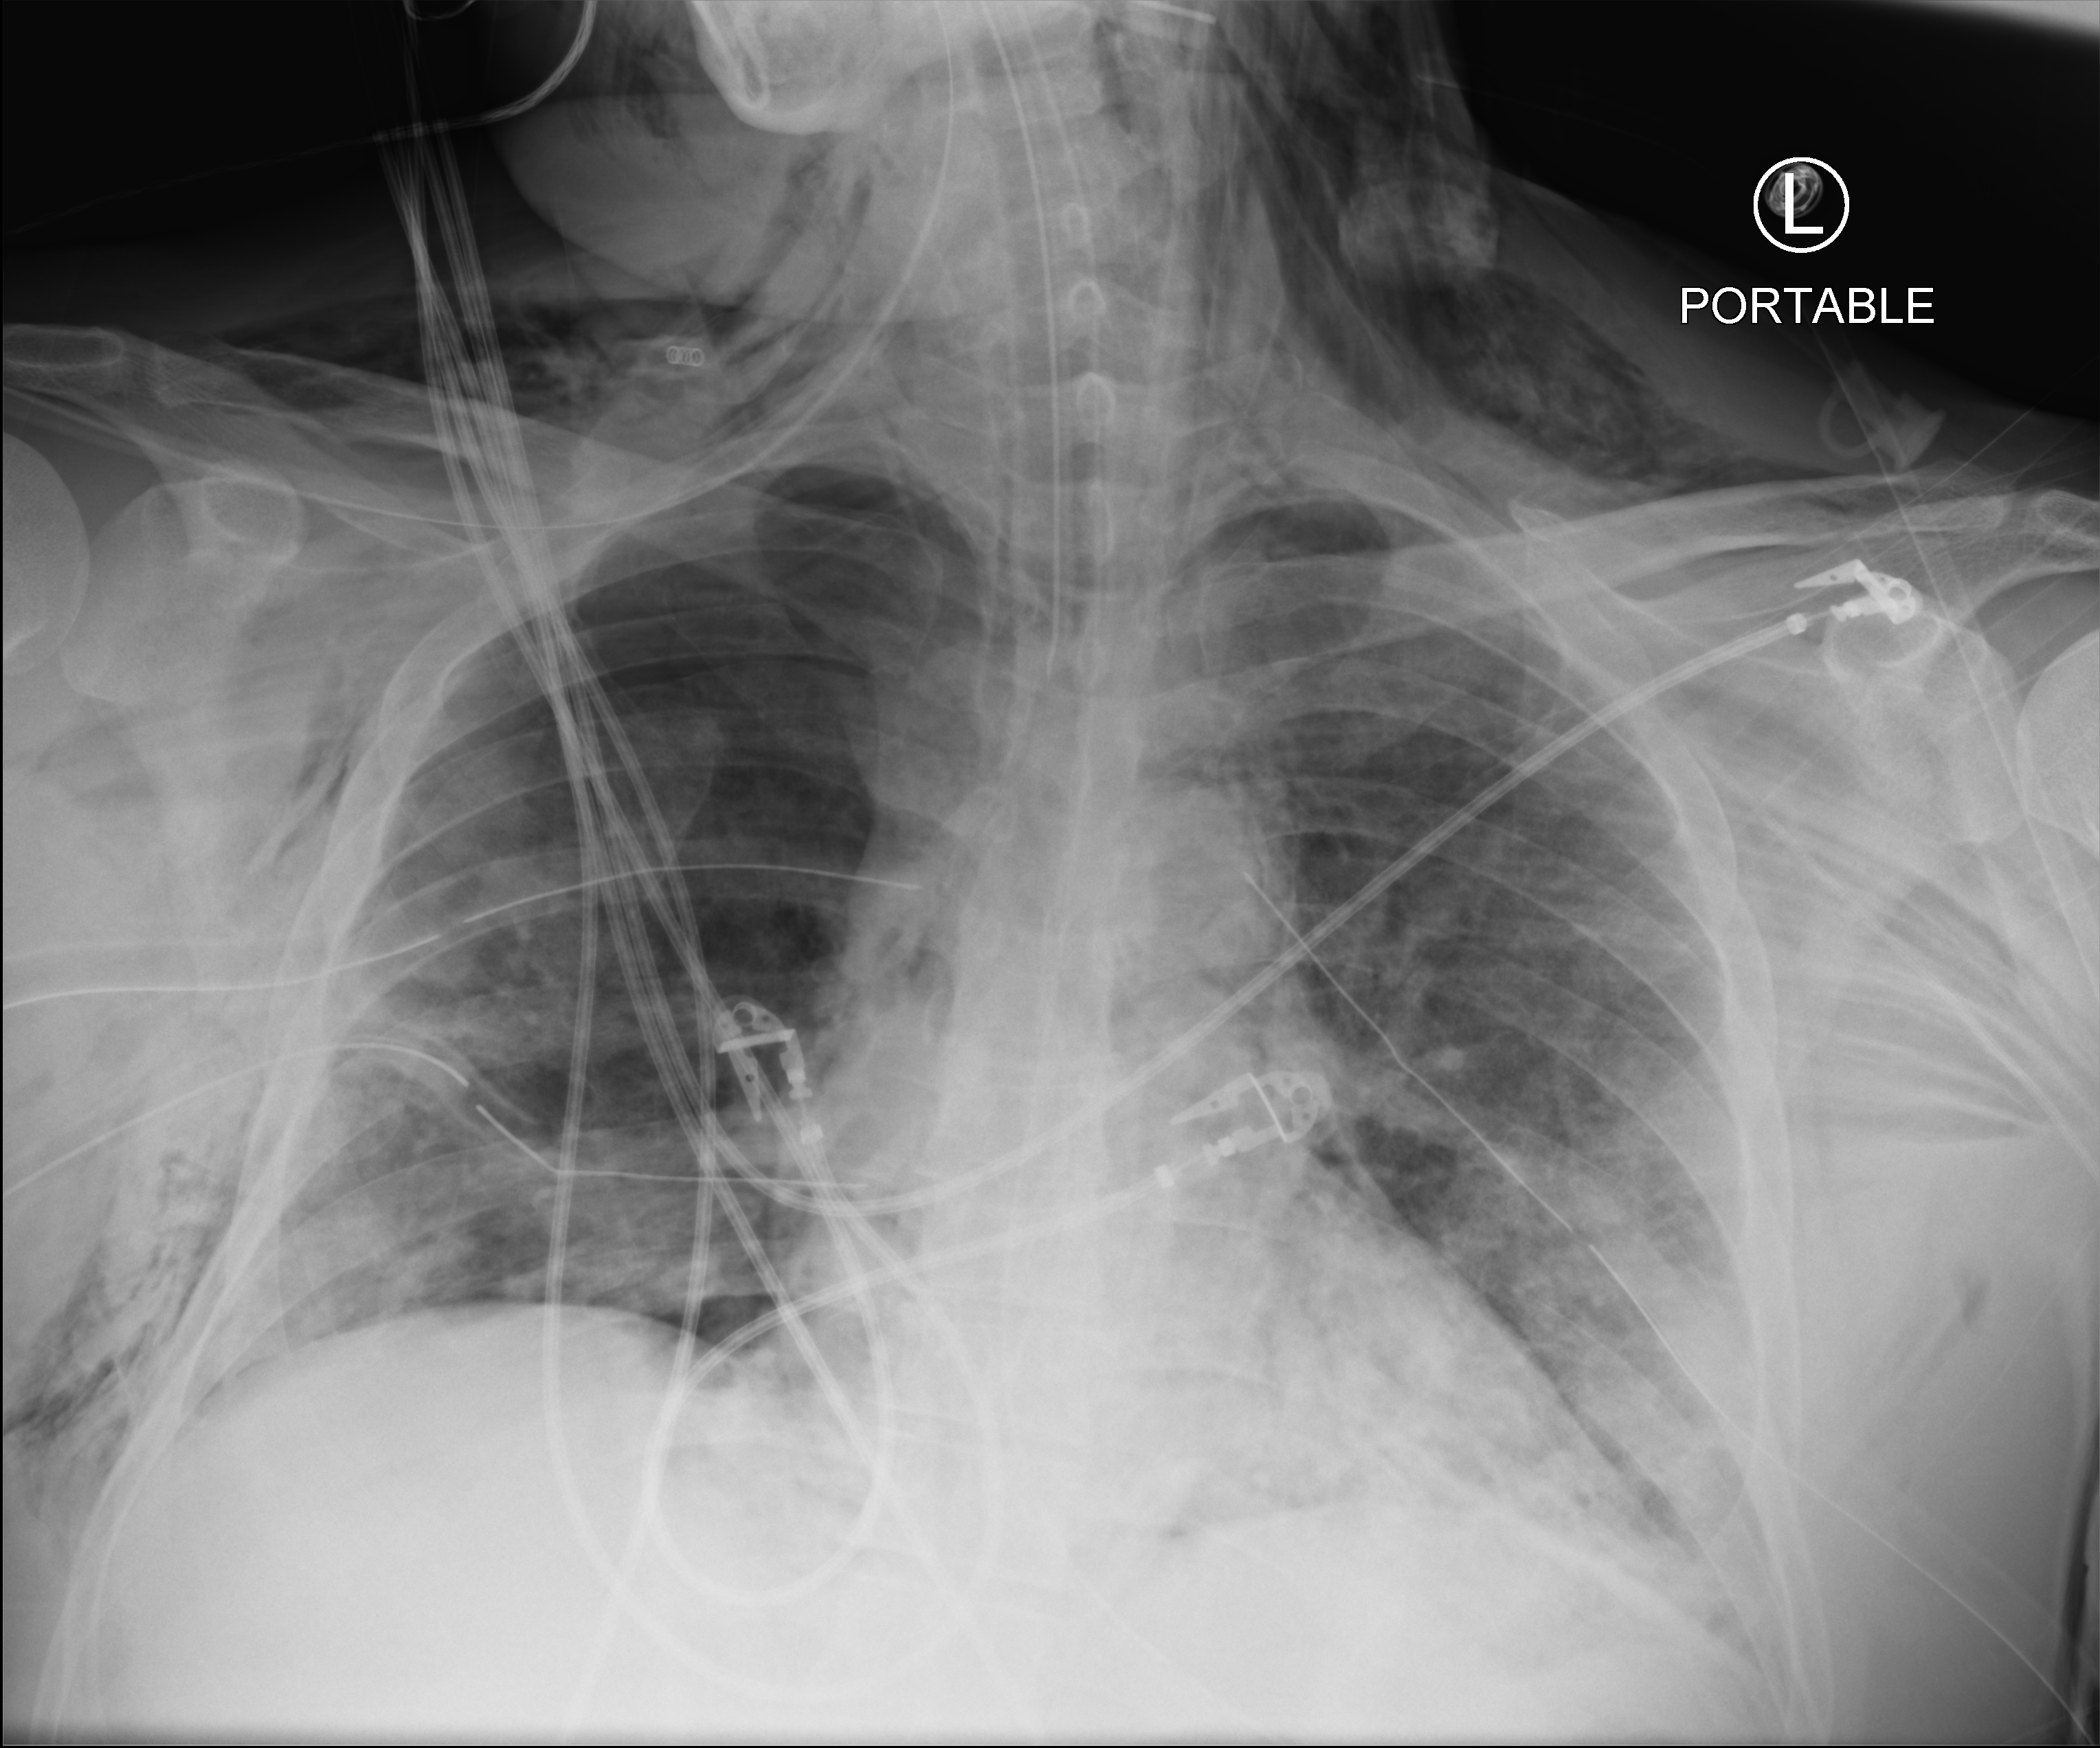
Bedside chest radiograph (computed radiography), anteroposterior (AP) projection. Patient hospitalised with COVID-19; male, aged 18–59 years.
From the hospital-stay record, not from the radiograph (when in the stay this image was taken is not recorded):
- admitted to intensive care during this hospital stay: yes